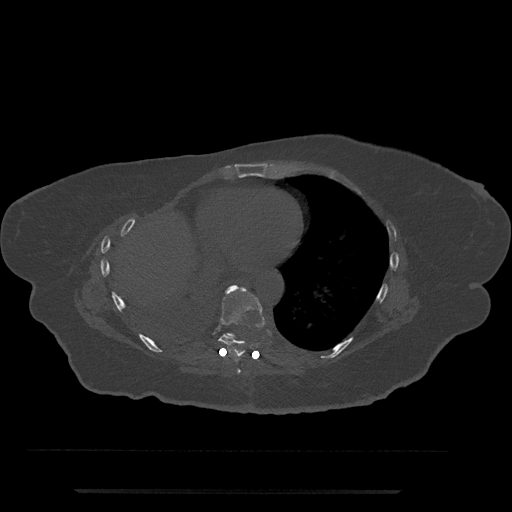
CT including the spine, one axial slice. Position 382 of 797 along the scan axis. Bone window (W 1800 / L 400 HU). 0.5 mm slice thickness. 512 × 512 image matrix. Patient: female, 51 years. From the clinical record (not read from this slice): primary cancer: neuro; vertebrae with lytic lesions (as recorded): T8.
Annotated regions visible in this slice (semi-automatic segmentation, software-assisted and operator-edited):
- T7 vertebra: bounding box (x1, y1, x2, y2) in pixels: (237, 369, 241, 374)
- T8 vertebra: (210, 285, 265, 358)
- T9 vertebra: (226, 333, 235, 340)